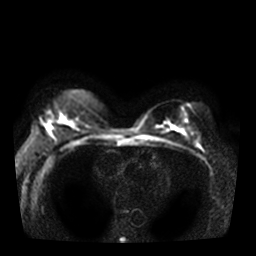
Breast MRI, one axial slice. Slice 18 of 36 in the series (ordered by position). Diffusion-weighted series; image 2 of 4 stored at this slice position (different b-values; order by instance number). 3 T. 5 mm slice thickness. 256 × 256 image matrix, field of view 330 × 330 mm. Female patient.
Annotated regions visible in this slice (outlined manually by an expert reader):
- tumour on diffusion-weighted imaging: bounding box [x1, y1, x2, y2] px = [67, 121, 76, 128]